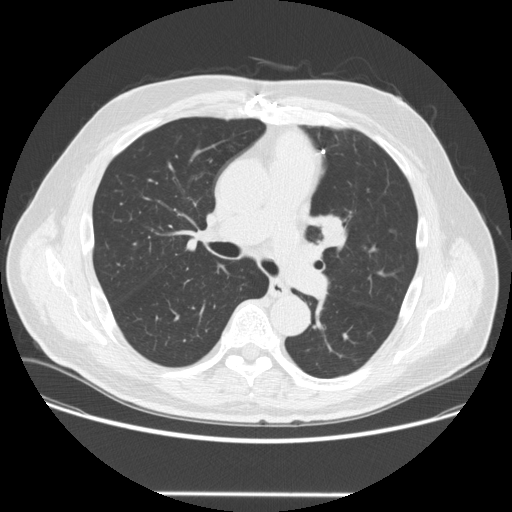
Axial slice from a low-dose chest CT screening exam. Third screening round (two years after baseline). Lung window (W 1500 / L -600 HU). Standard (soft-tissue) reconstruction kernel (STANDARD). Male participant, aged 66 years at enrolment.
- Expert reader's lesion annotation, bounding box <305,207,357,255> (left, top, right, bottom; pixels).
- The screening reader recorded 2 non-calcified nodules or masses ≥4 mm on this exam; which of them this box marks is not recorded.
- Official screen result: positive, other.